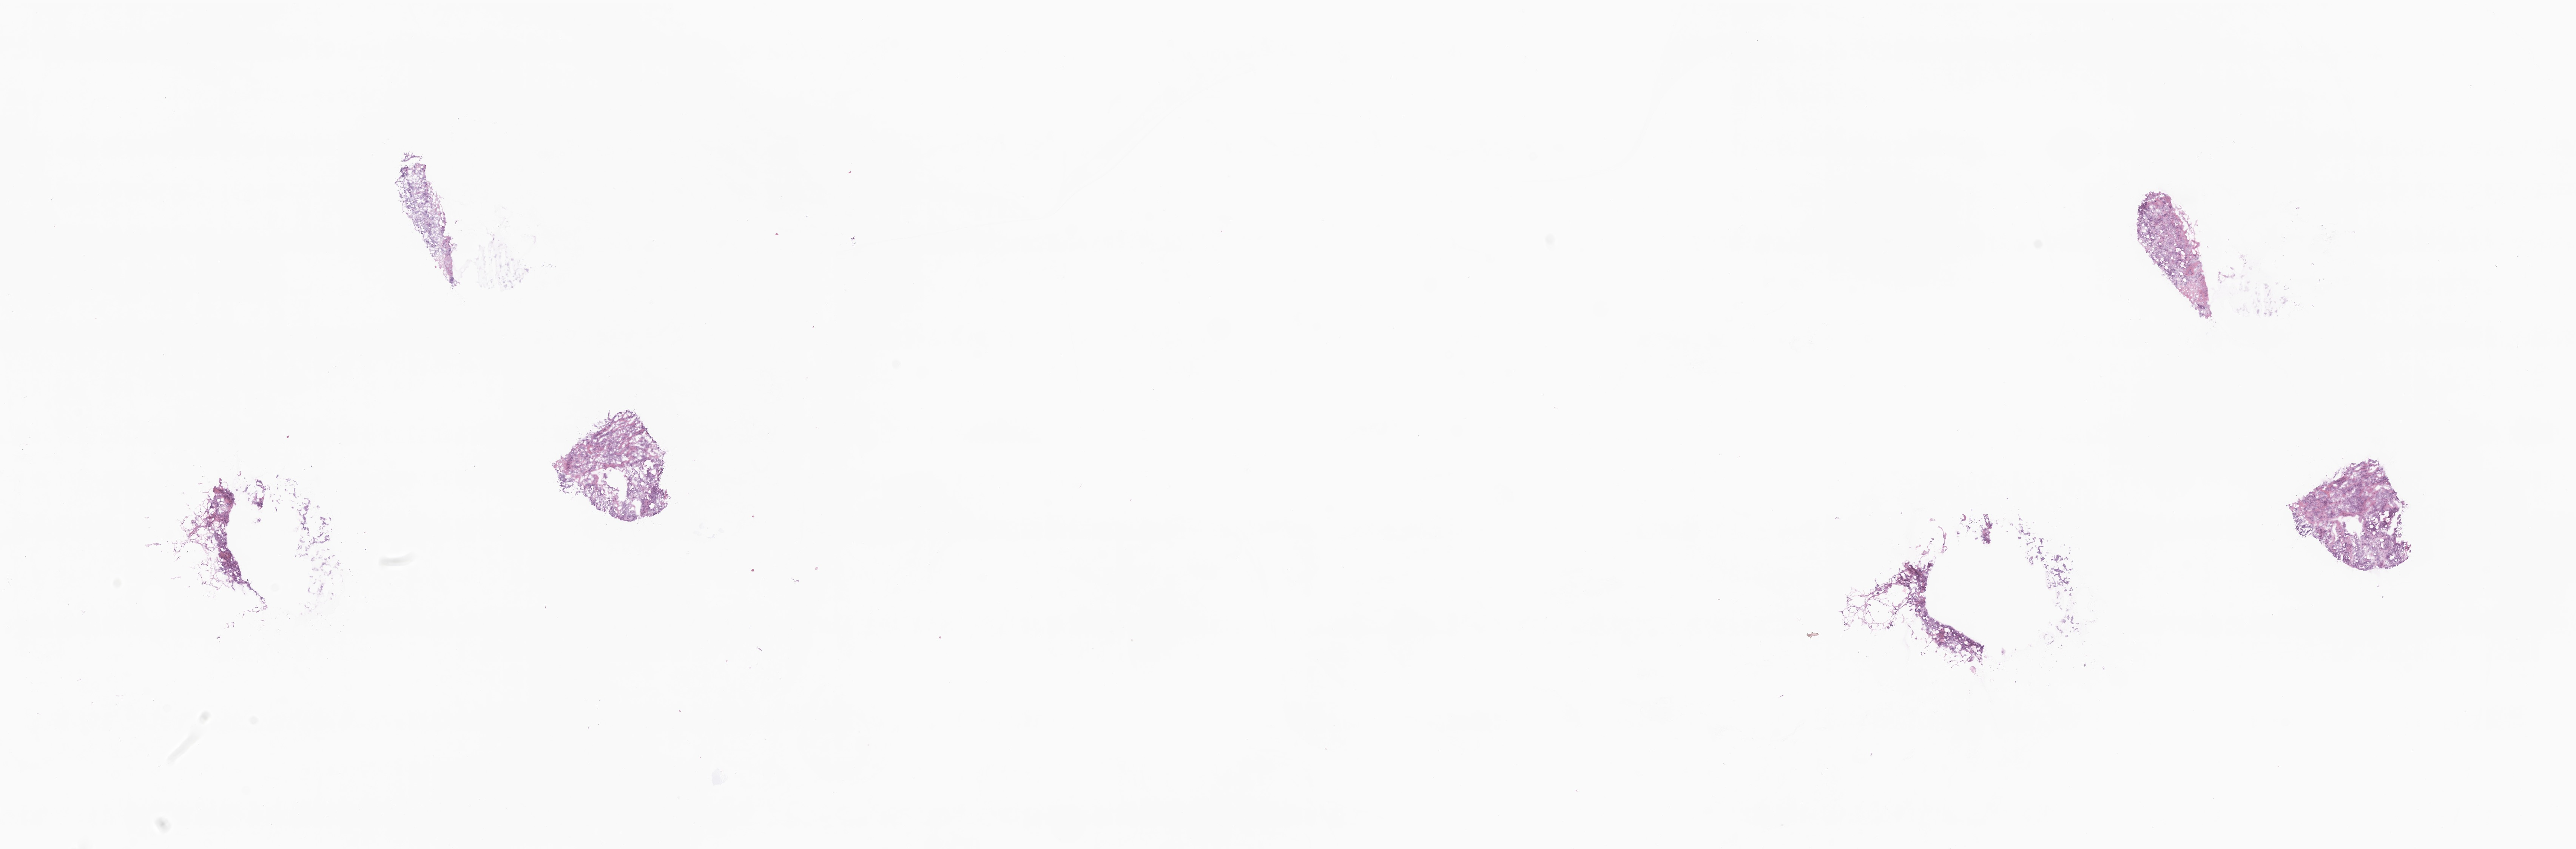
Hematoxylin and eosin (H&E) whole-slide image — low-resolution overview of the scanned area, about 28.8 x 9.5 mm; frozen section (tissue freezing medium); specimen: primary tumor; anatomic site: breast (right). Patient: female, age at initial diagnosis 76 years. Pathologist review of this section (percent, as recorded): tumor cells 85%, tumor nuclei 85%, stromal cells 15%, necrosis 0%, normal cells 0%. Infiltration values recorded for this section: lymphocyte infiltration 0%, monocyte infiltration 0%, neutrophil infiltration 0%.
Diagnosis: Infiltrating duct carcinoma, NOS.